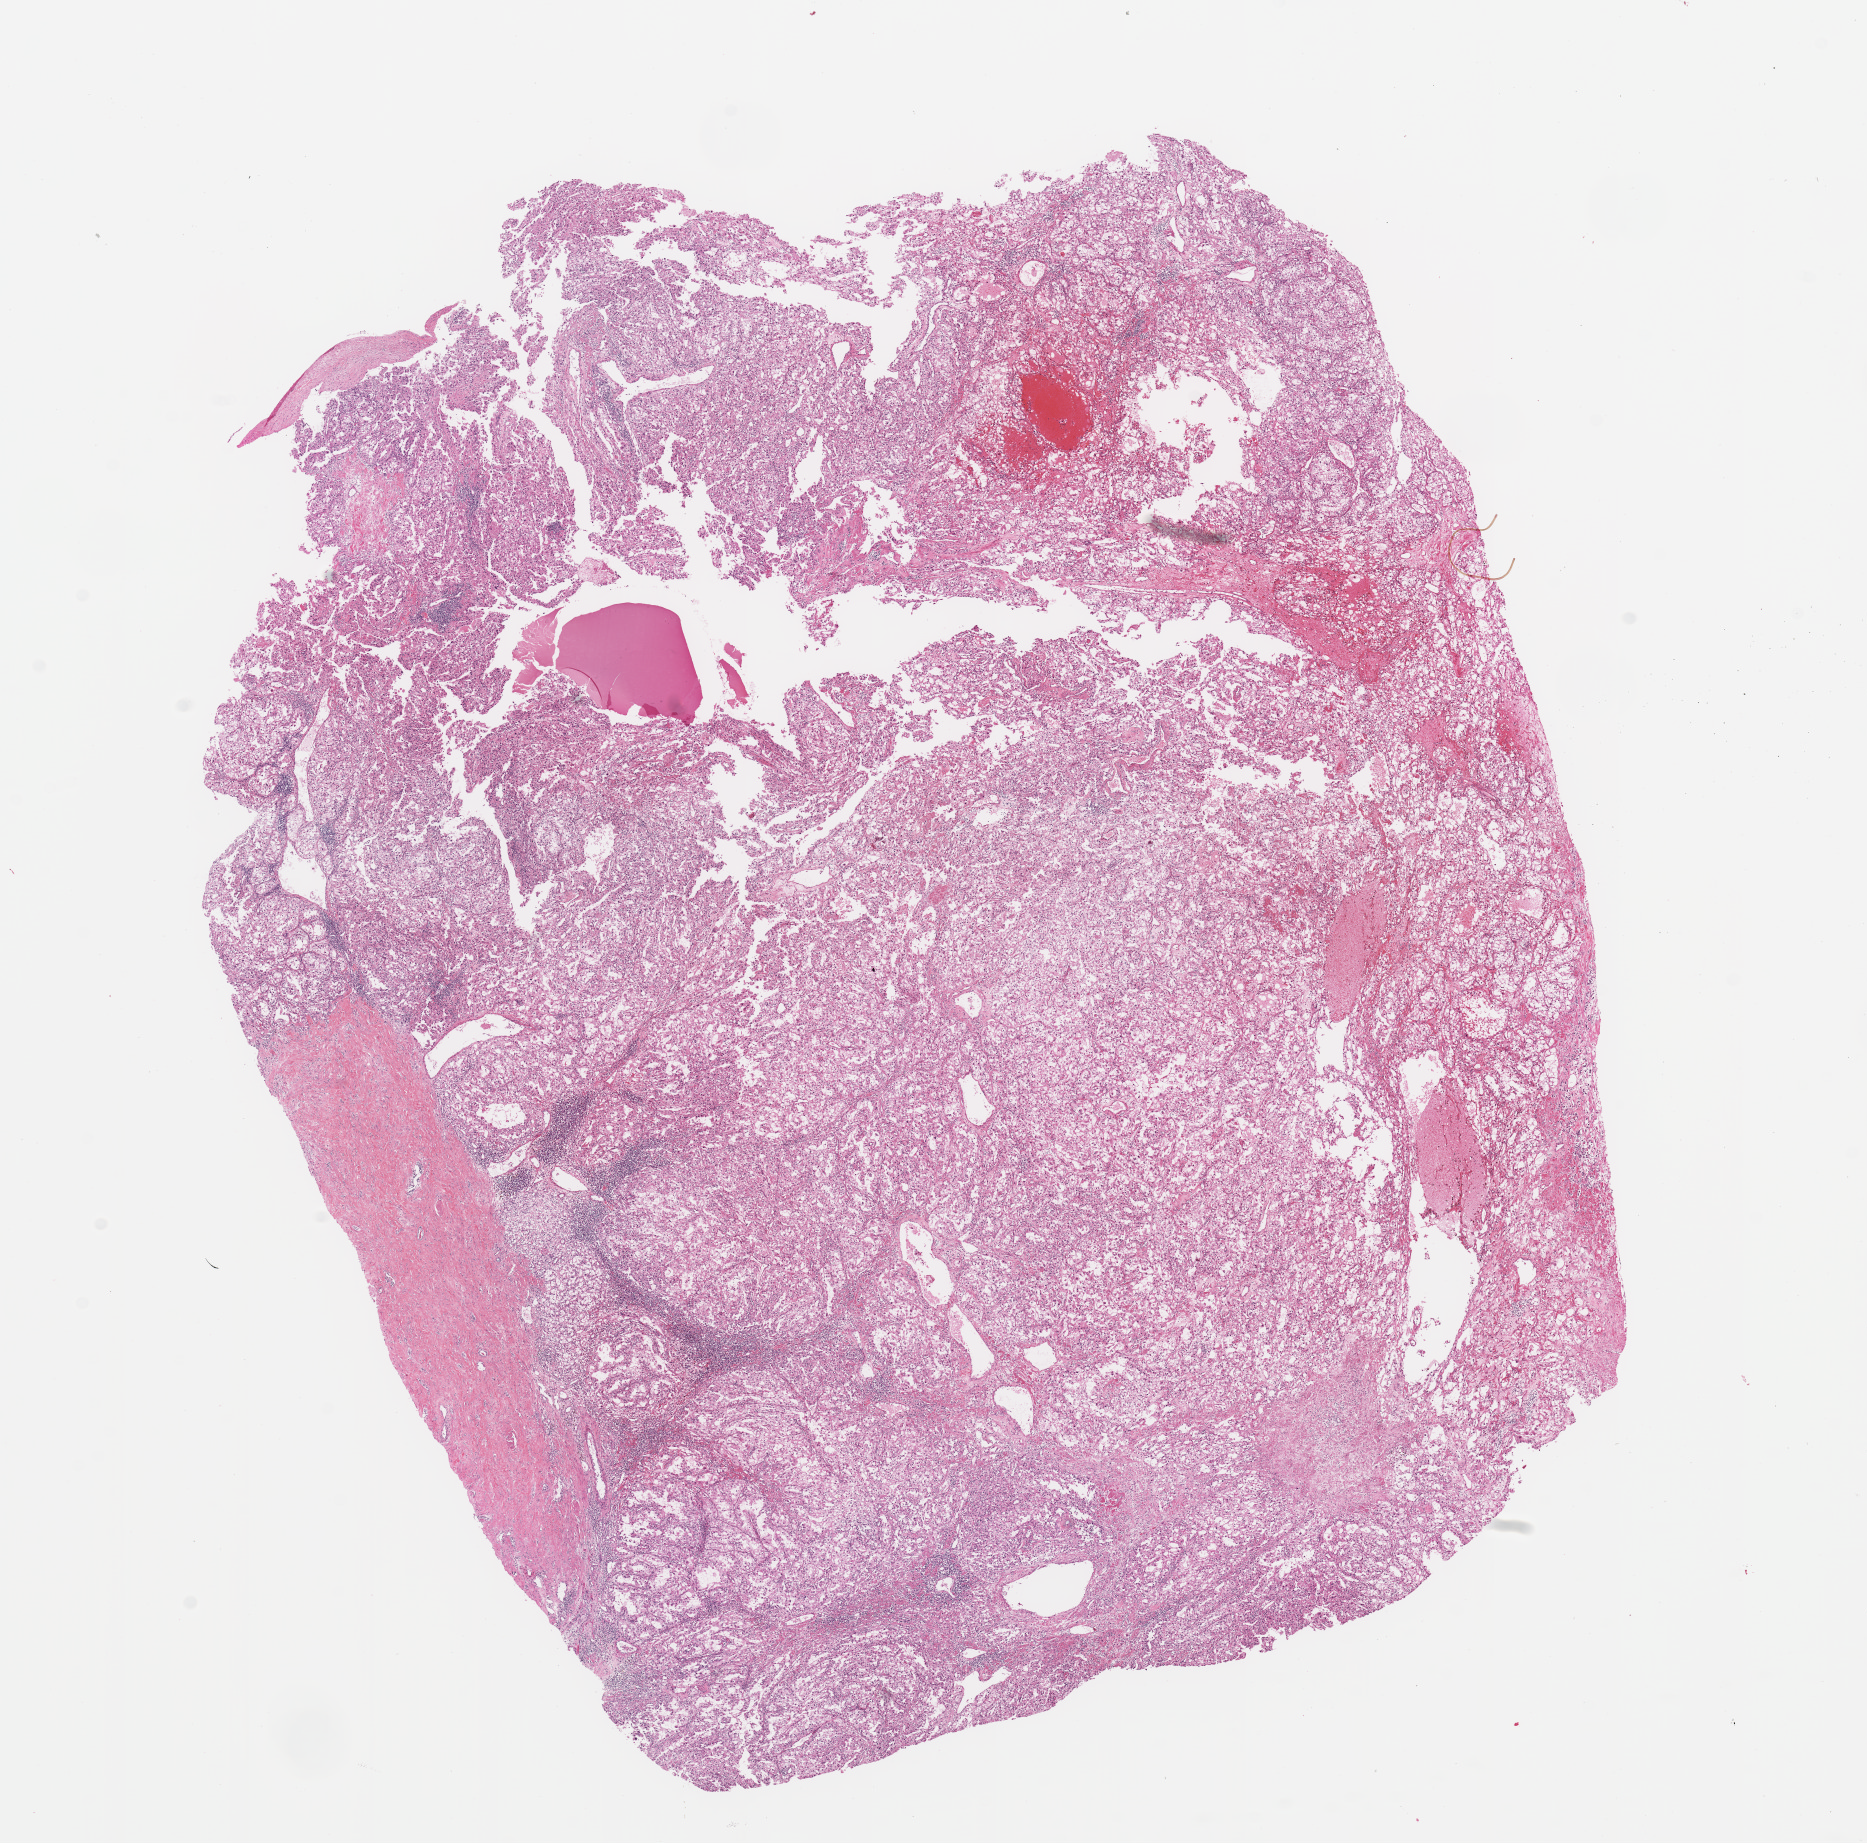
H&E-stained whole-slide image — whole scanned area (about 14.8 x 14.6 mm, slide scanned at 20x) shown as a low-resolution overview. Tumour tissue sample, sampled site: kidney. 67-year-old male patient. Histologic grade: G2 (moderately differentiated). Pathologist review of this section (percent, as recorded): tumour nuclei 80%, necrosis 5%.
- primary tumour site (as recorded): upper pole
- histologic diagnosis: Renal cell carcinoma, NOS
- AJCC pathologic stage: I